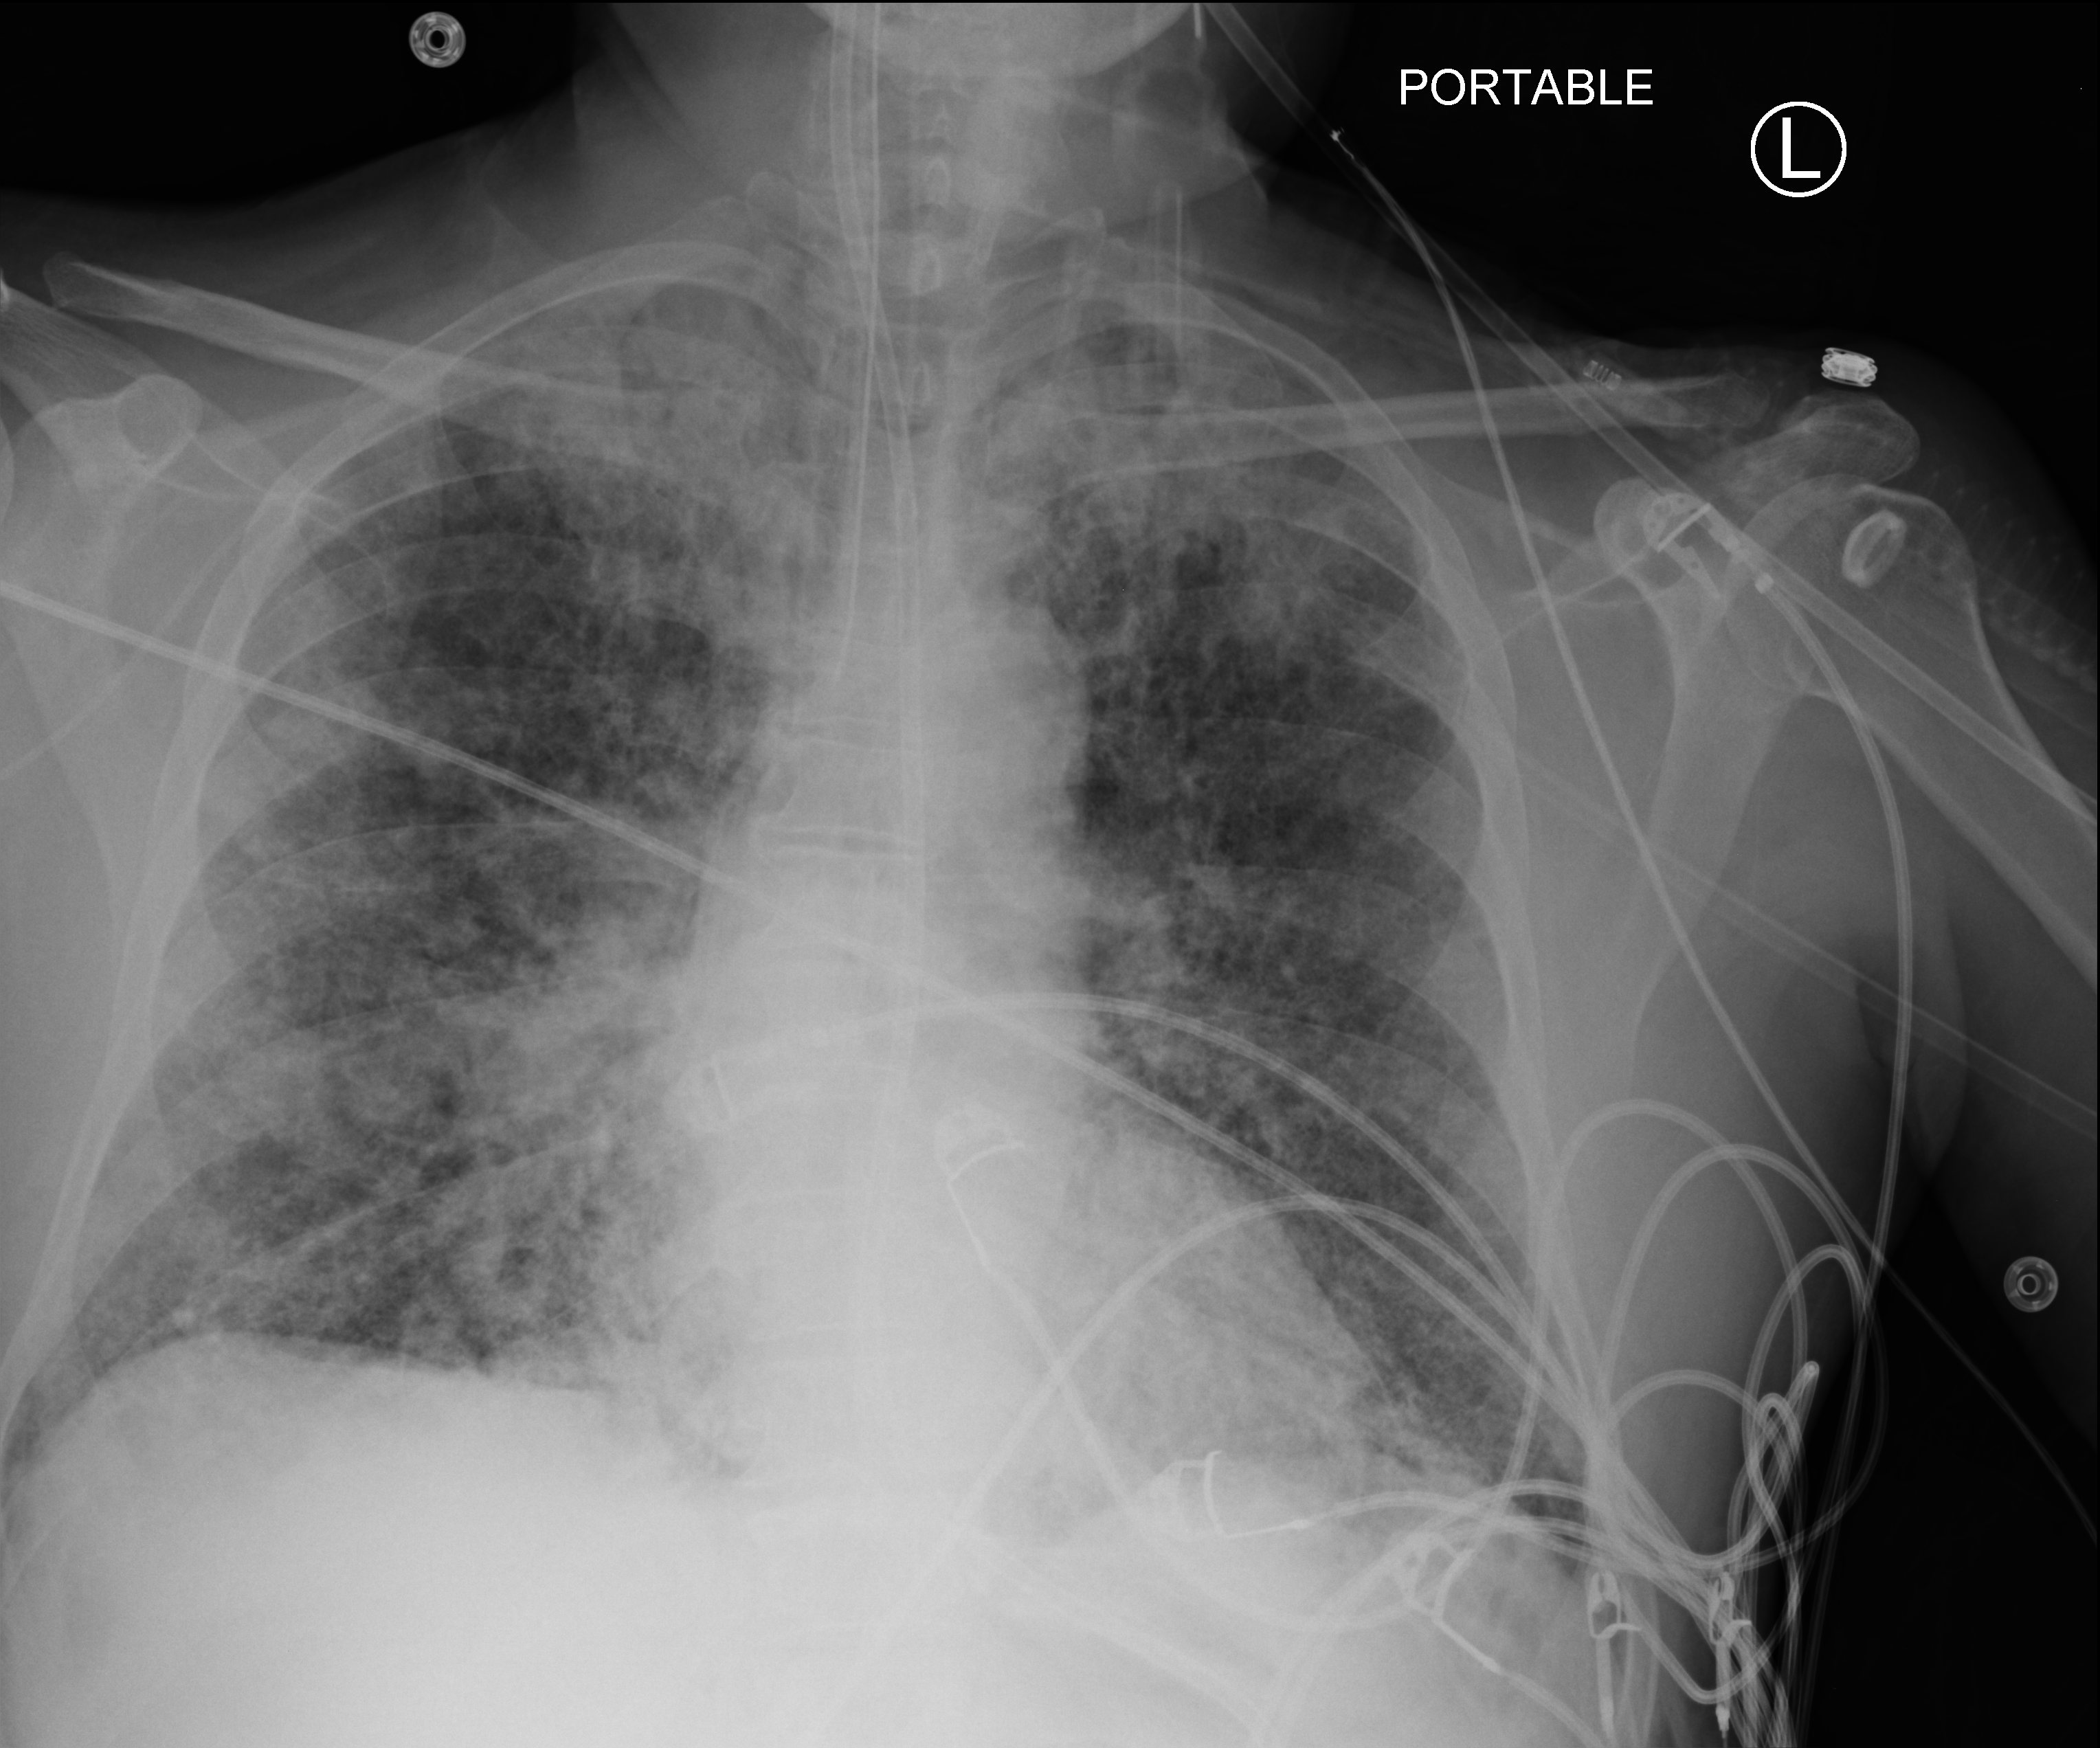
Portable chest radiograph, anteroposterior (AP) projection. Male patient hospitalised with COVID-19, age 18–59 years.
Hospital-stay facts (about this admission, not read from this image; timing relative to this image not recorded):
- admitted to intensive care during this hospital stay: yes